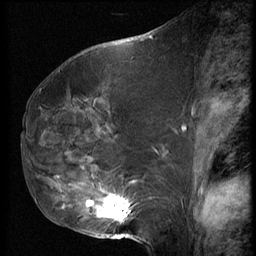
Breast MRI (dynamic contrast-enhanced), one sagittal slice; position 32 of 62 along the scan axis; 3 images stored at this slice position (order not interpretable as contrast timing); 1.5 T; TE 4.2 ms, TR 9 ms; 2.5 mm slice thickness; 256 × 256 image matrix, field of view 180 × 180 mm. Patient: female, 50 years. Case-level facts recorded for this patient, not image findings: setting: breast cancer imaged before/during neoadjuvant chemotherapy; receptor status: HR-positive, HER2-negative.
Structures marked on this image (semi-automatic segmentation, software-assisted and operator-edited):
- analysis volume of interest (the breast-tissue region the enhancement analysis was run in; not a lesion): bounding box <59,125,139,238> (left, top, right, bottom; pixels)
- tumour enhancement mask (voxels above the 140 % enhancement threshold inside the analysis volume of interest): <89,195,131,220>